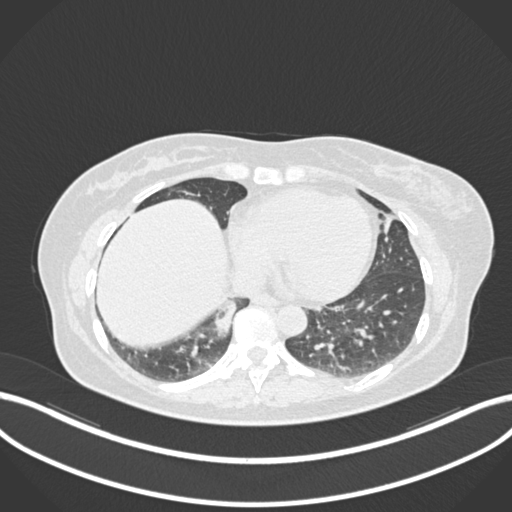
Chest CT, one axial slice. 120 kVp. Lung window (W 1500 / L -600 HU). 512 × 512 image matrix, field of view 400 × 400 mm. Patient: female, 54 years. From the clinical record (not read from this slice): clinical TNM (as recorded): T4 N0 M0.
Annotated regions visible in this slice (rectangle marked by the reading radiologist):
- lung tumour (recorded histology: adenocarcinoma): bounding box <211,292,236,345> (left, top, right, bottom; pixels)